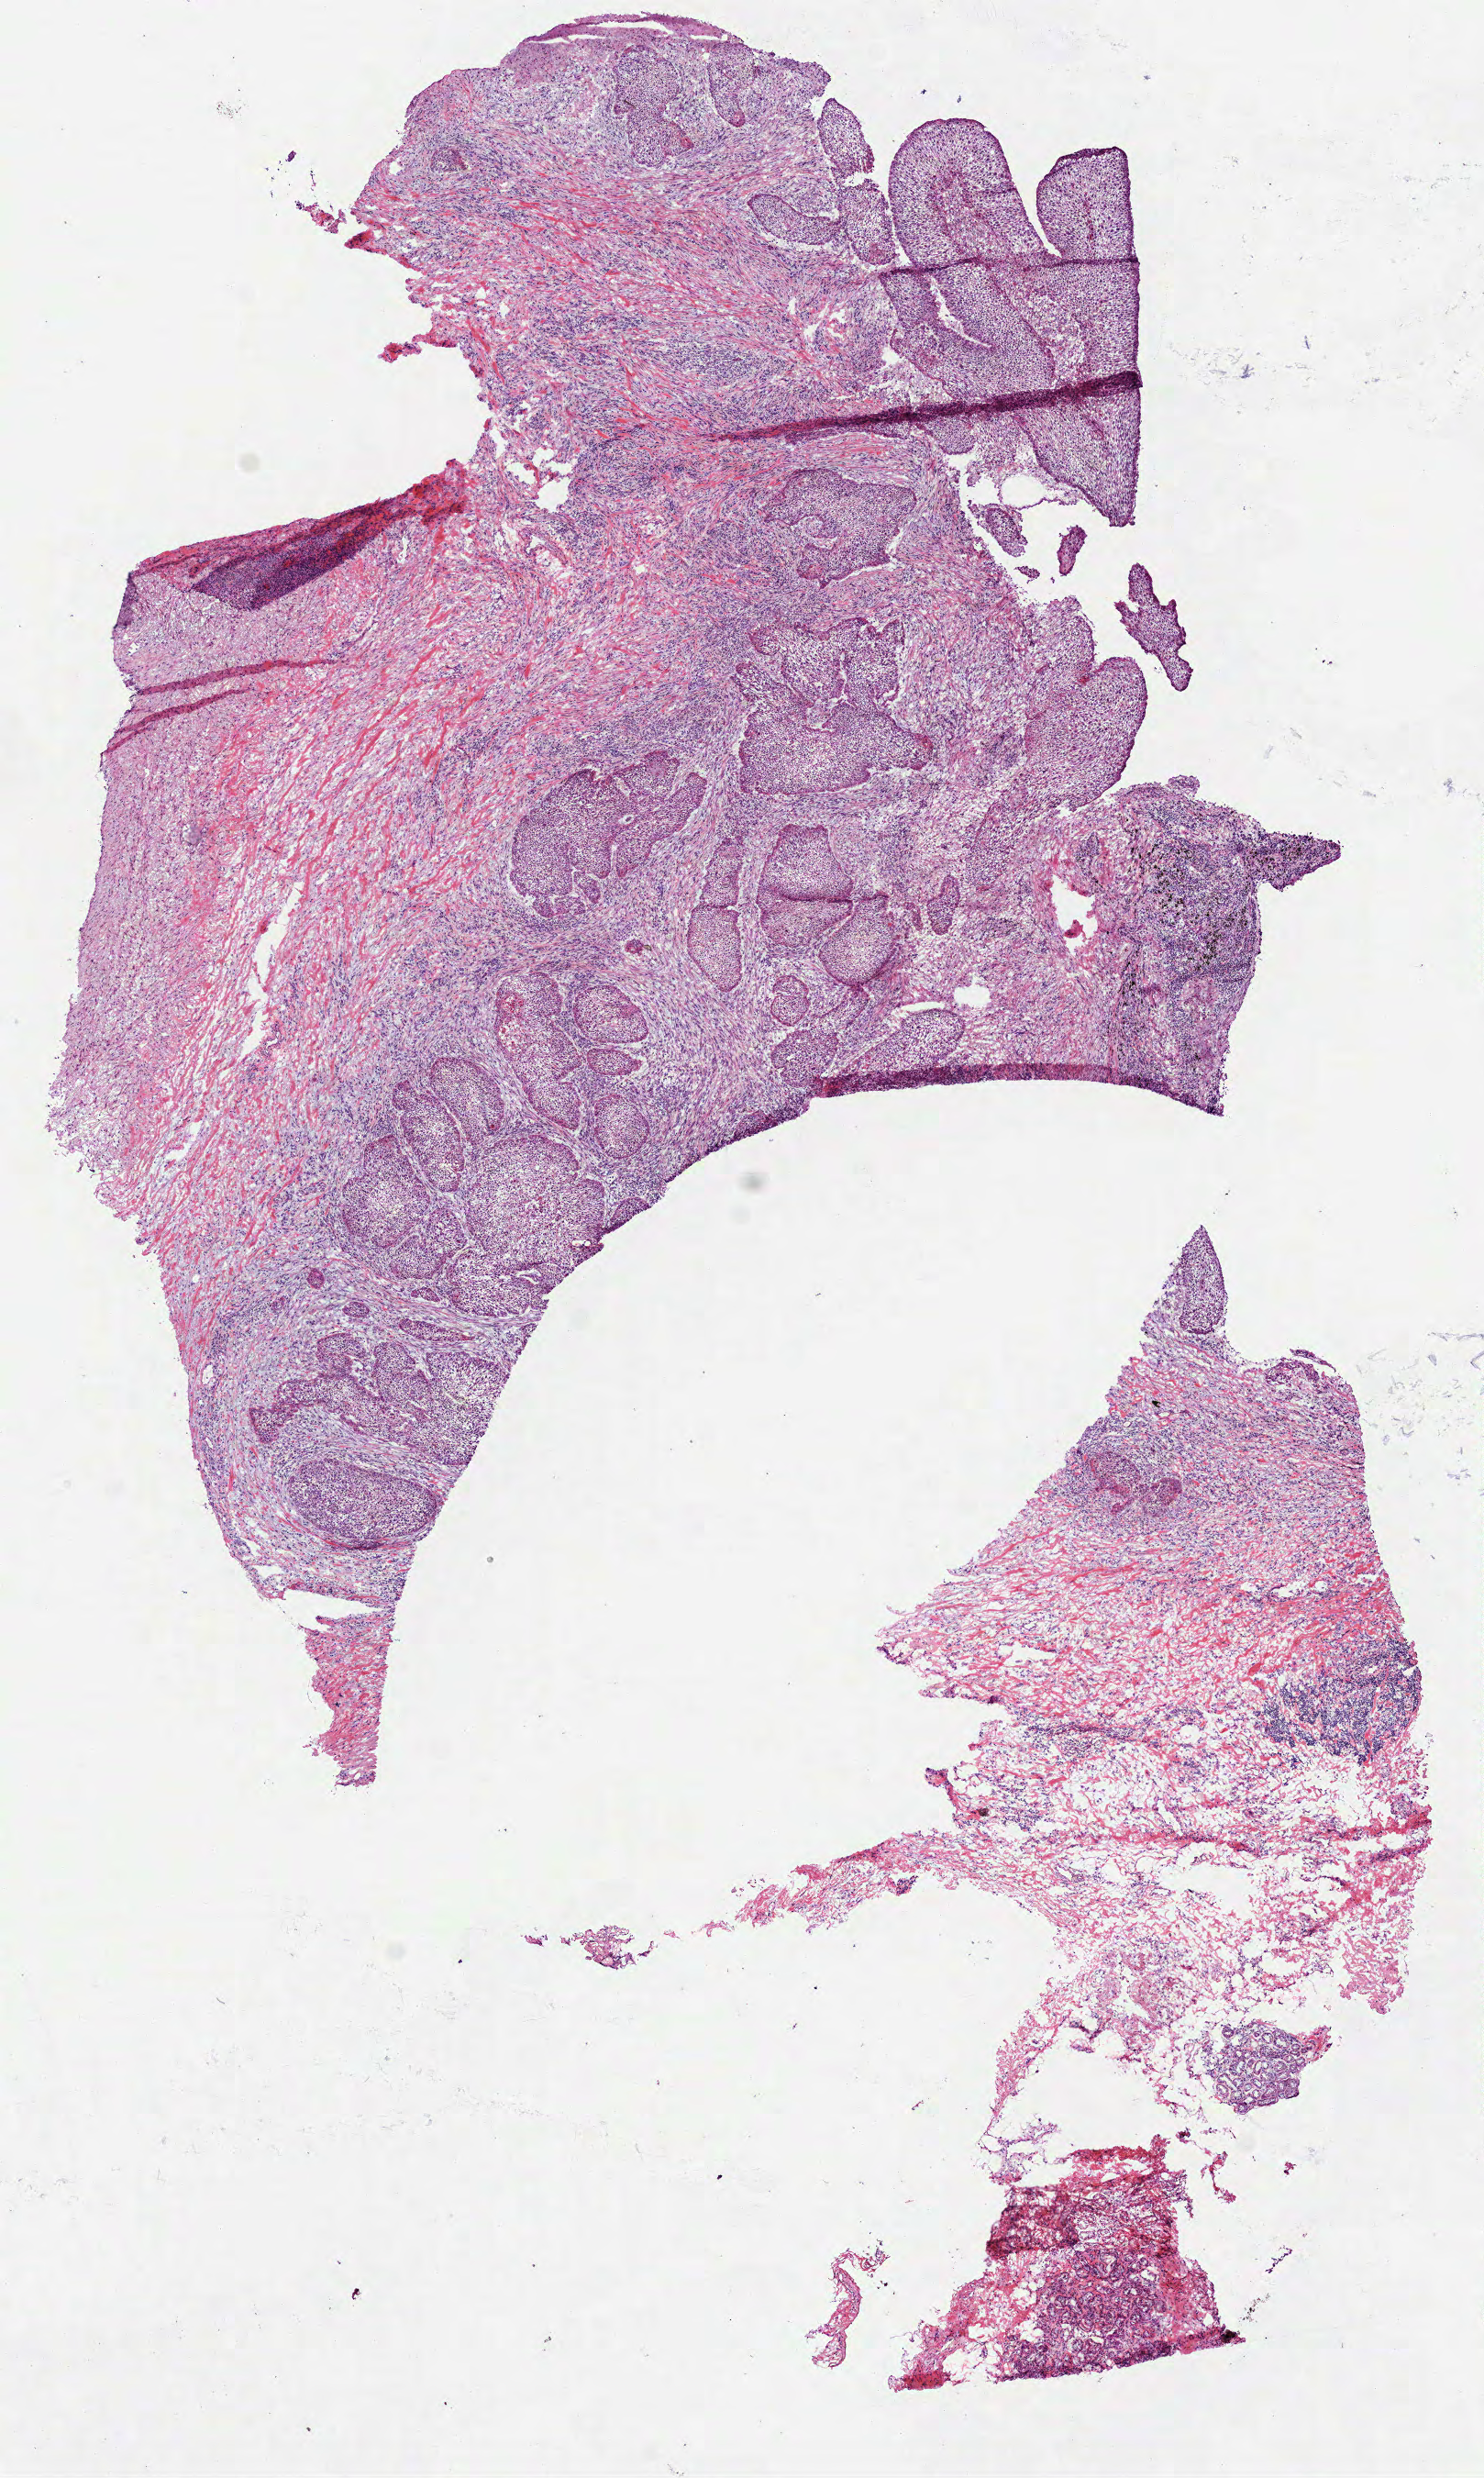
H&E whole-slide image, a low-resolution overview of the entire scanned area, about 6.5 x 10.9 mm (acquisition: 40x scan). Frozen section. Lung, primary tumour sample. Male, age 83 years at initial diagnosis. Slide review estimates, as recorded: tumour cells 45%, tumour nuclei 40%, normal cells 5%, stromal cells 50%, necrosis 0%. Inflammatory infiltration, as recorded: lymphocyte infiltration 20%, monocyte infiltration 1%, neutrophil infiltration 1%.
Laterality: left. AJCC pathologic stage: IIB. TNM: T2 N1 MX. Histologic diagnosis: Squamous cell carcinoma, NOS (lower lobe, lung).